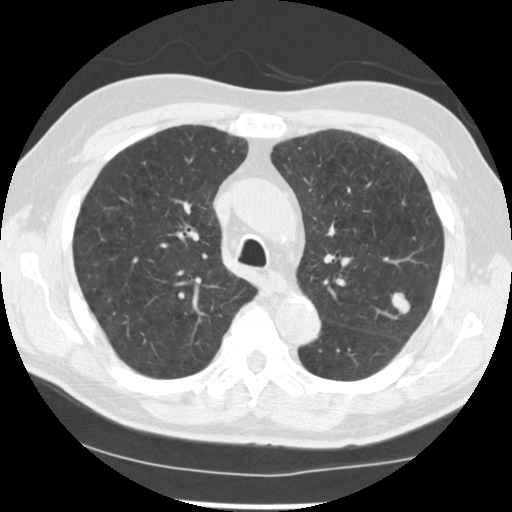
Low-dose screening chest CT, axial slice. Baseline screening round. Lung window (W 1500 / L -600 HU). Slice 171 of 249 in the series. Male, age 71 years at enrolment. Current smoker at enrolment.
- Expert reader's lesion annotation, box from (x=380, y=283) to (x=424, y=329) px.
- The screening reader recorded 2 non-calcified nodules or masses ≥4 mm on this exam; which of them this box marks is not recorded.
- Participant outcome: lung cancer diagnosed 37 days after this screen — adenocarcinoma, NOS, left upper lobe, poorly differentiated (G3), stage IIIB (AJCC 6th edition), 25 mm at pathology.